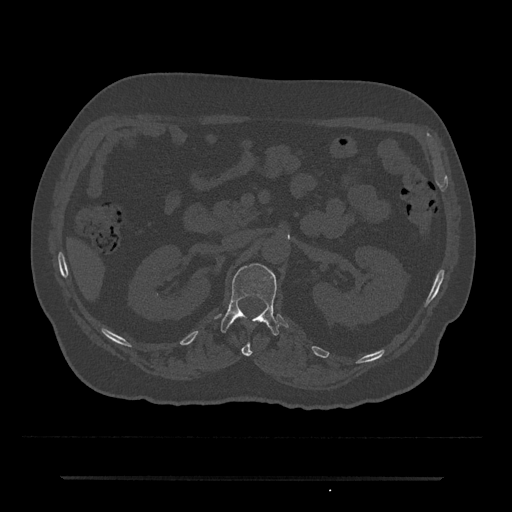
CT including the spine, one axial slice. Bone window (W 1800 / L 400 HU). 0.5 mm slice thickness. 512 × 512 image matrix, field of view 437 × 437 mm. Male patient, age 69 years. Case-level facts recorded for this patient, not image findings: primary cancer: prostate.
Annotated regions visible in this slice (semi-automatic segmentation, software-assisted and operator-edited):
- L1 vertebra: bounding box [x1, y1, x2, y2] px = [220, 263, 279, 336]
- T12 vertebra: [241, 342, 252, 356]